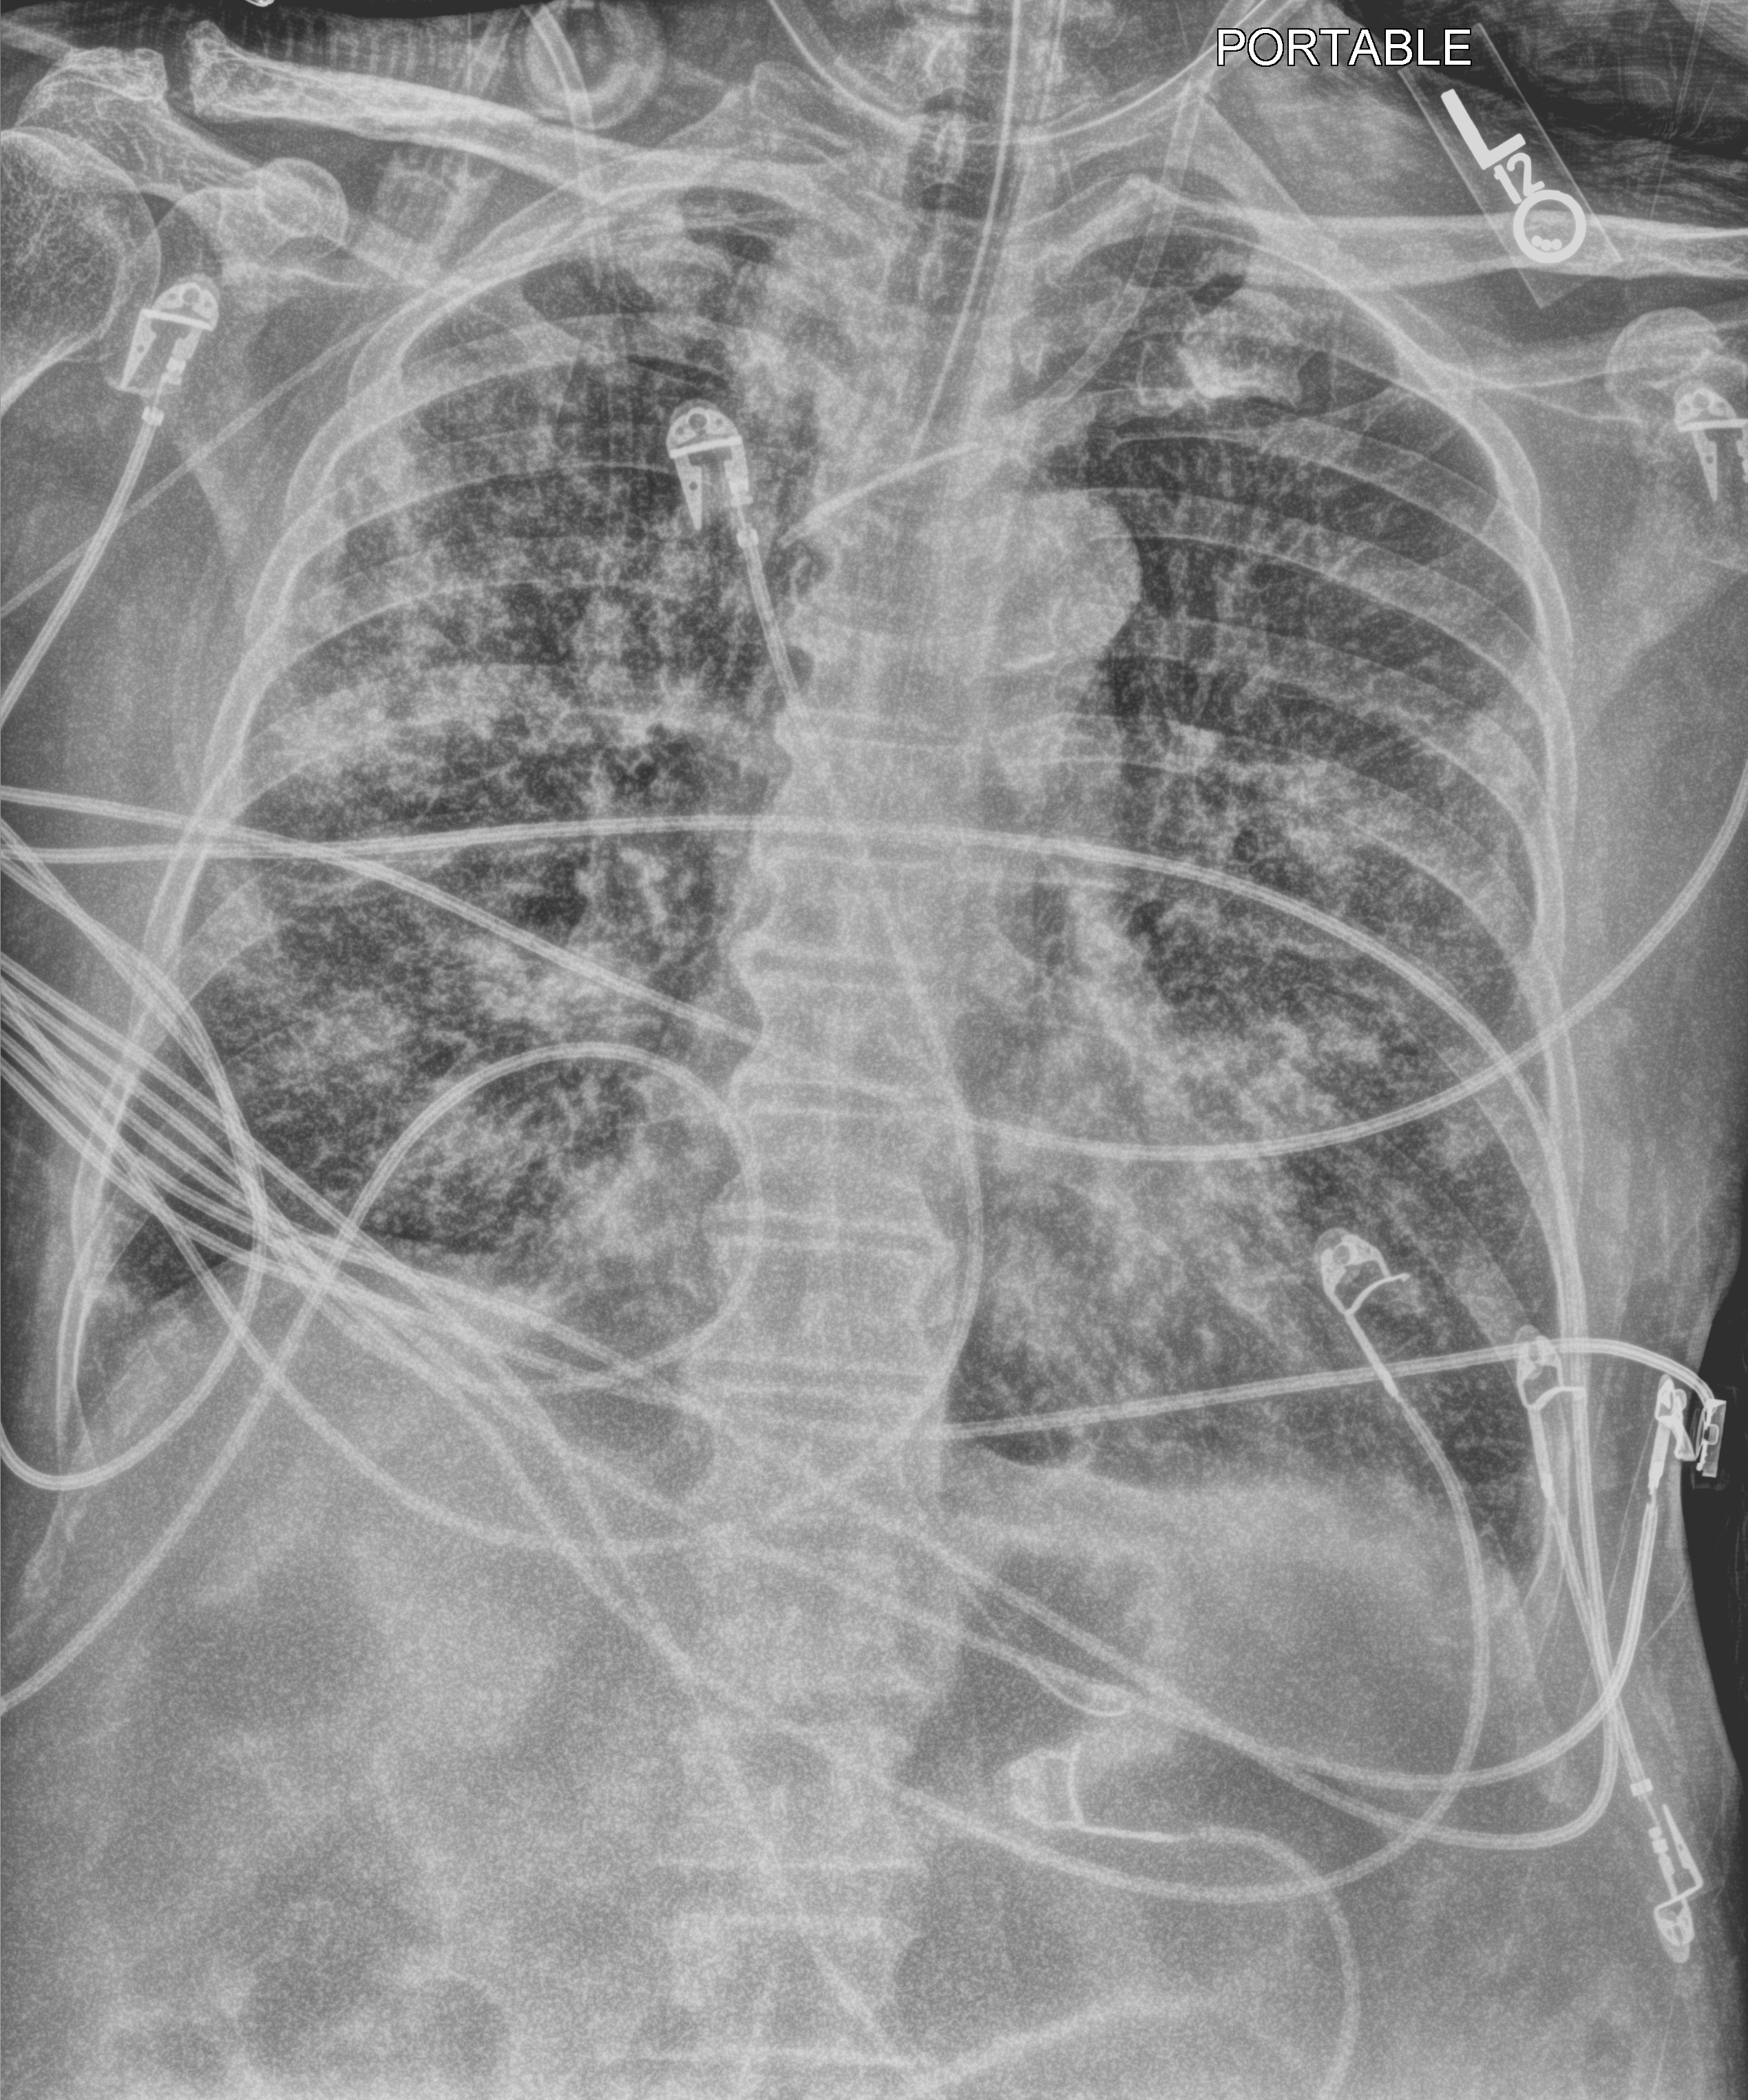
Chest X-ray (portable), anteroposterior (AP) projection. Patient hospitalised with COVID-19; male, aged 60–74 years.
Admission-level facts for this patient (not findings on this image; timing relative to this image not recorded): COPD (admission record): no.